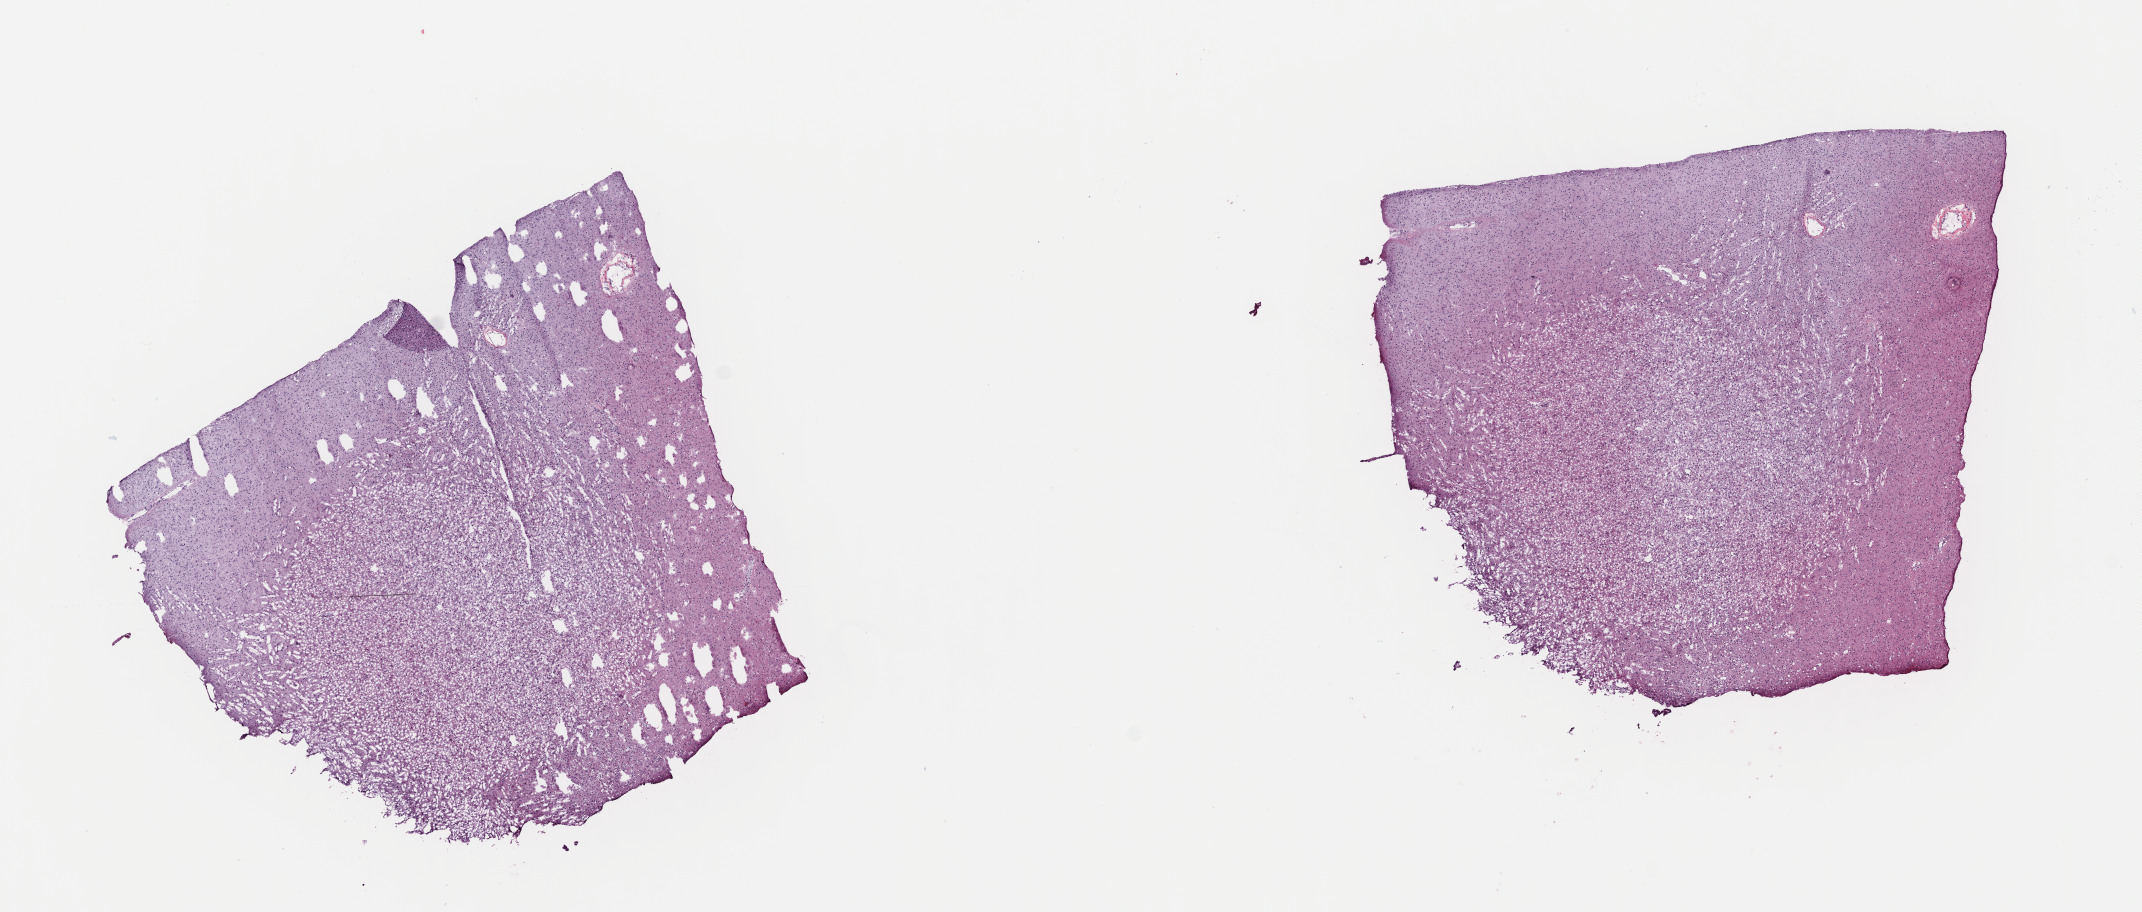
Digitized H&E tissue section (whole slide), low-resolution overview of the scanned area, about 16.9 x 7.2 mm, frozen section from the top of the tissue portion, primary tumour sample from the brain. Male, age 33 years at initial diagnosis. Histologic grade: G2 (moderately differentiated). Pathologist review of this section (percent, as recorded): tumour cells 40%, tumour nuclei 80%, normal cells 10%, stromal cells 50%, necrosis 0%. Infiltration values recorded for this section: lymphocyte infiltration 0%, monocyte infiltration 0%, neutrophil infiltration 0%.
Pathologic diagnosis: Astrocytoma, NOS (cerebrum). Laterality: right.